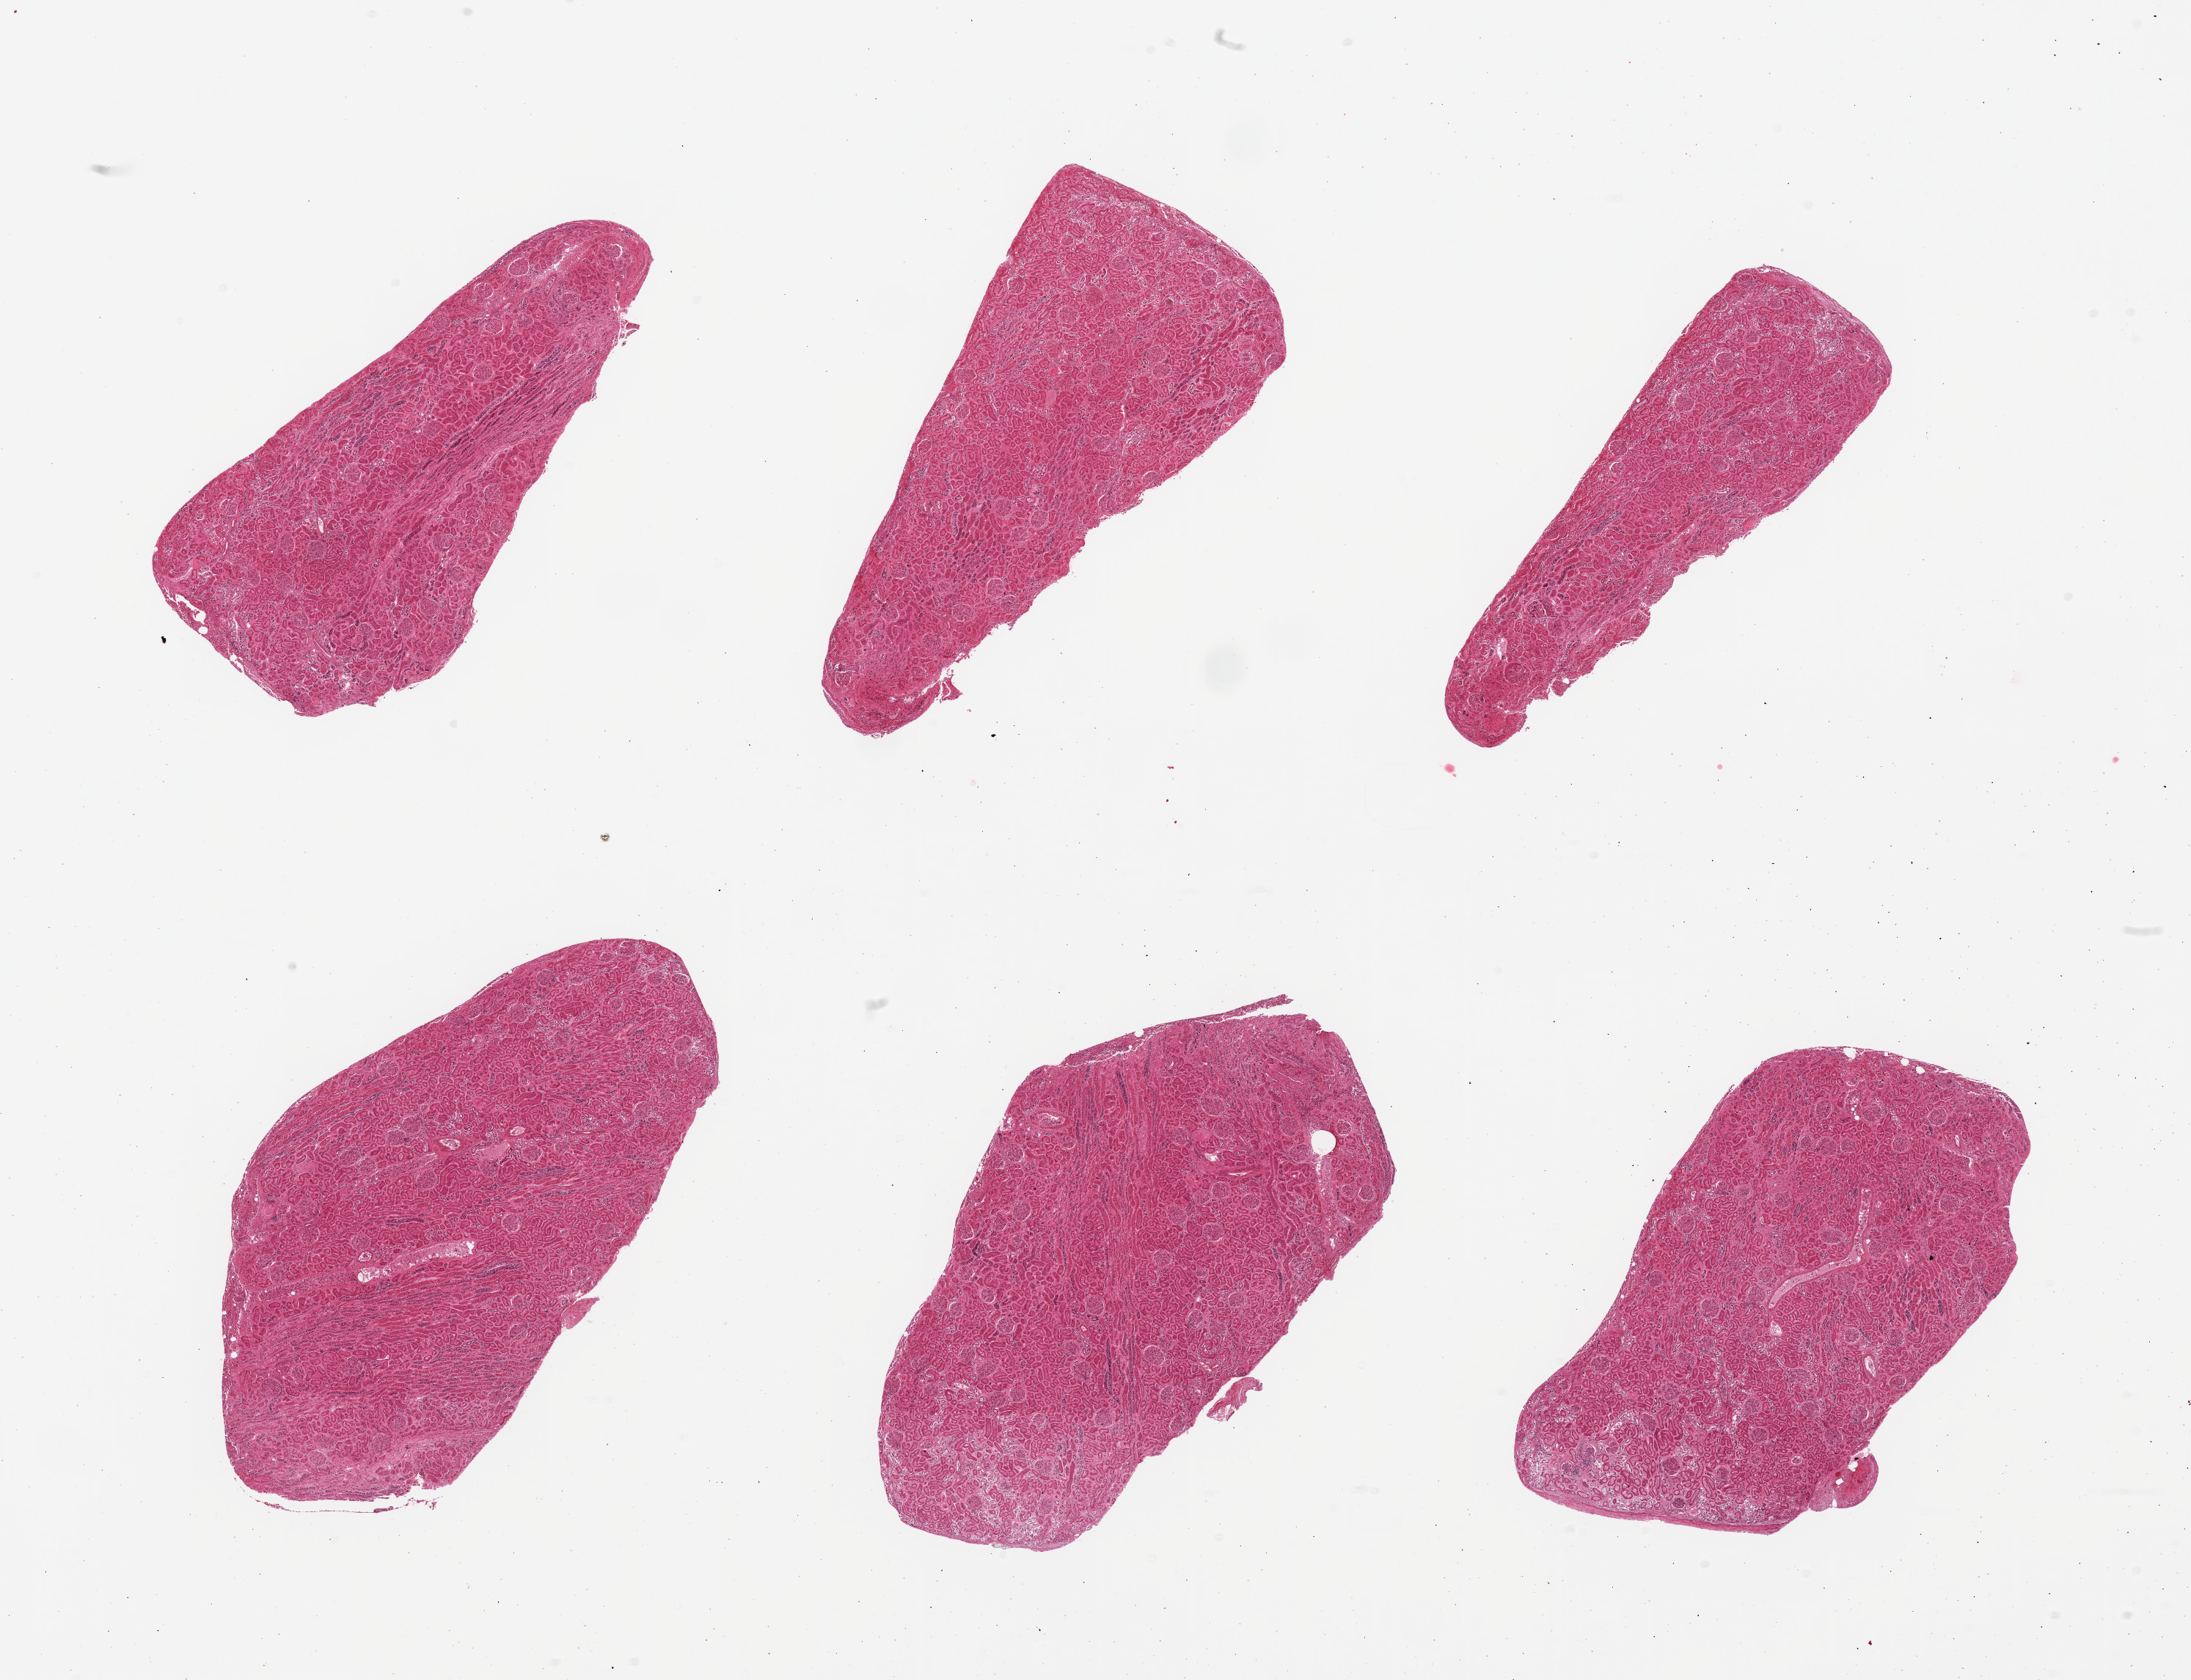
Digitized hematoxylin and eosin (H&E)-stained section, a low-resolution overview of the entire scanned area, about 23.6 x 18.1 mm; PAXgene-fixed, paraffin-embedded tissue; sampled site (target tissue): renal cortex; tissue donor sample. Donor: female.
Reviewer comment on this tissue sample: 6 pieces, confirmed target muscularis.